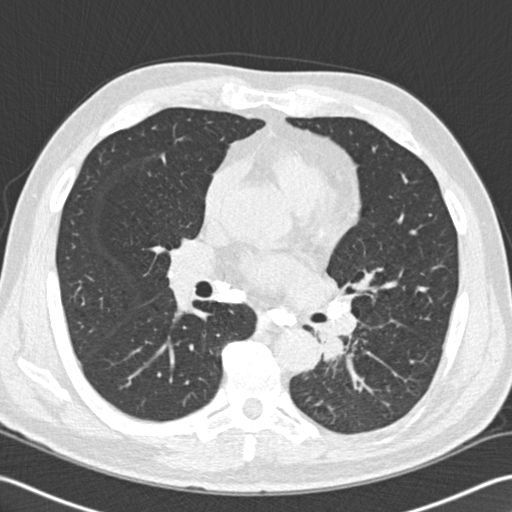
Low-dose screening chest CT, one axial slice; position 93 of 170 along the scan axis; reconstruction kernel B30f; lung window (W 1500 / L -600 HU); 512 × 512 image matrix.
Annotated regions visible in this slice (expert manual segmentation):
- lesion 1 (tumor, lower lobe of left lung): bounding box [x1, y1, x2, y2] px = [314, 322, 345, 361]